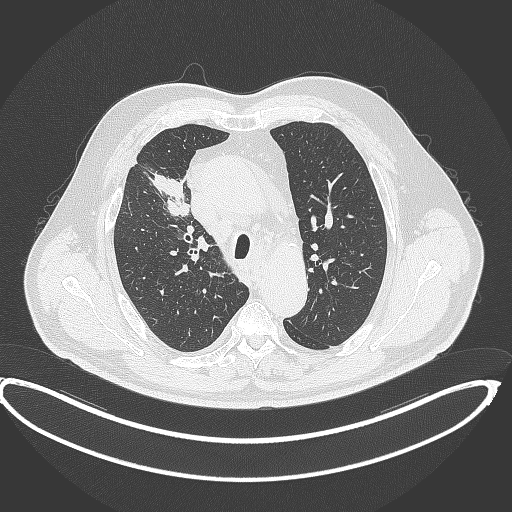
Chest CT, one axial slice. Position 291 of 390 along the scan axis. 120 kVp. Lung window (W 1500 / L -600 HU). 512 × 512 image matrix. Male patient, age 62 years. Case-level facts recorded for this patient, not image findings: clinical TNM (as recorded): T1c N3 M1c.
Outlined on this slice (bounding box drawn by a radiologist):
- lung tumour (recorded histology: adenocarcinoma): bounding box <145,169,192,219> (left, top, right, bottom; pixels)